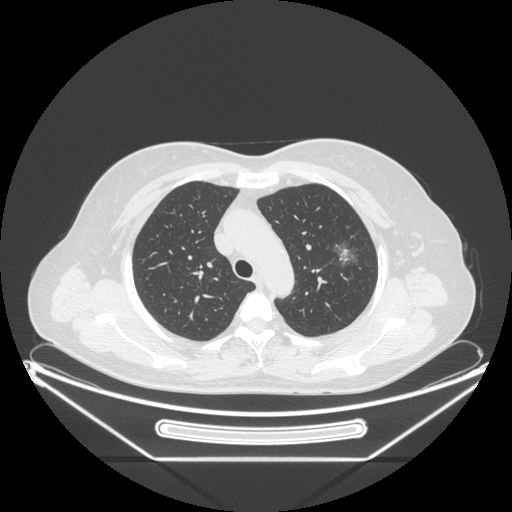
Chest CT, one axial slice. Position 161 of 226 along the scan axis. Reconstruction kernel STANDARD. 120 kVp. Lung window (W 1500 / L -600 HU). 1.25 mm slice thickness. 512 × 512 image matrix, field of view 447 × 447 mm. Patient: female, 54 years. From the clinical record (not read from this slice): clinical TNM (as recorded): T1c N0 M0; histopathological grade: G1.
Structures marked on this image (rectangle marked by the reading radiologist):
- lung tumour (recorded histology: adenocarcinoma): bounding box (x1, y1, x2, y2) in pixels: (329, 235, 362, 278)